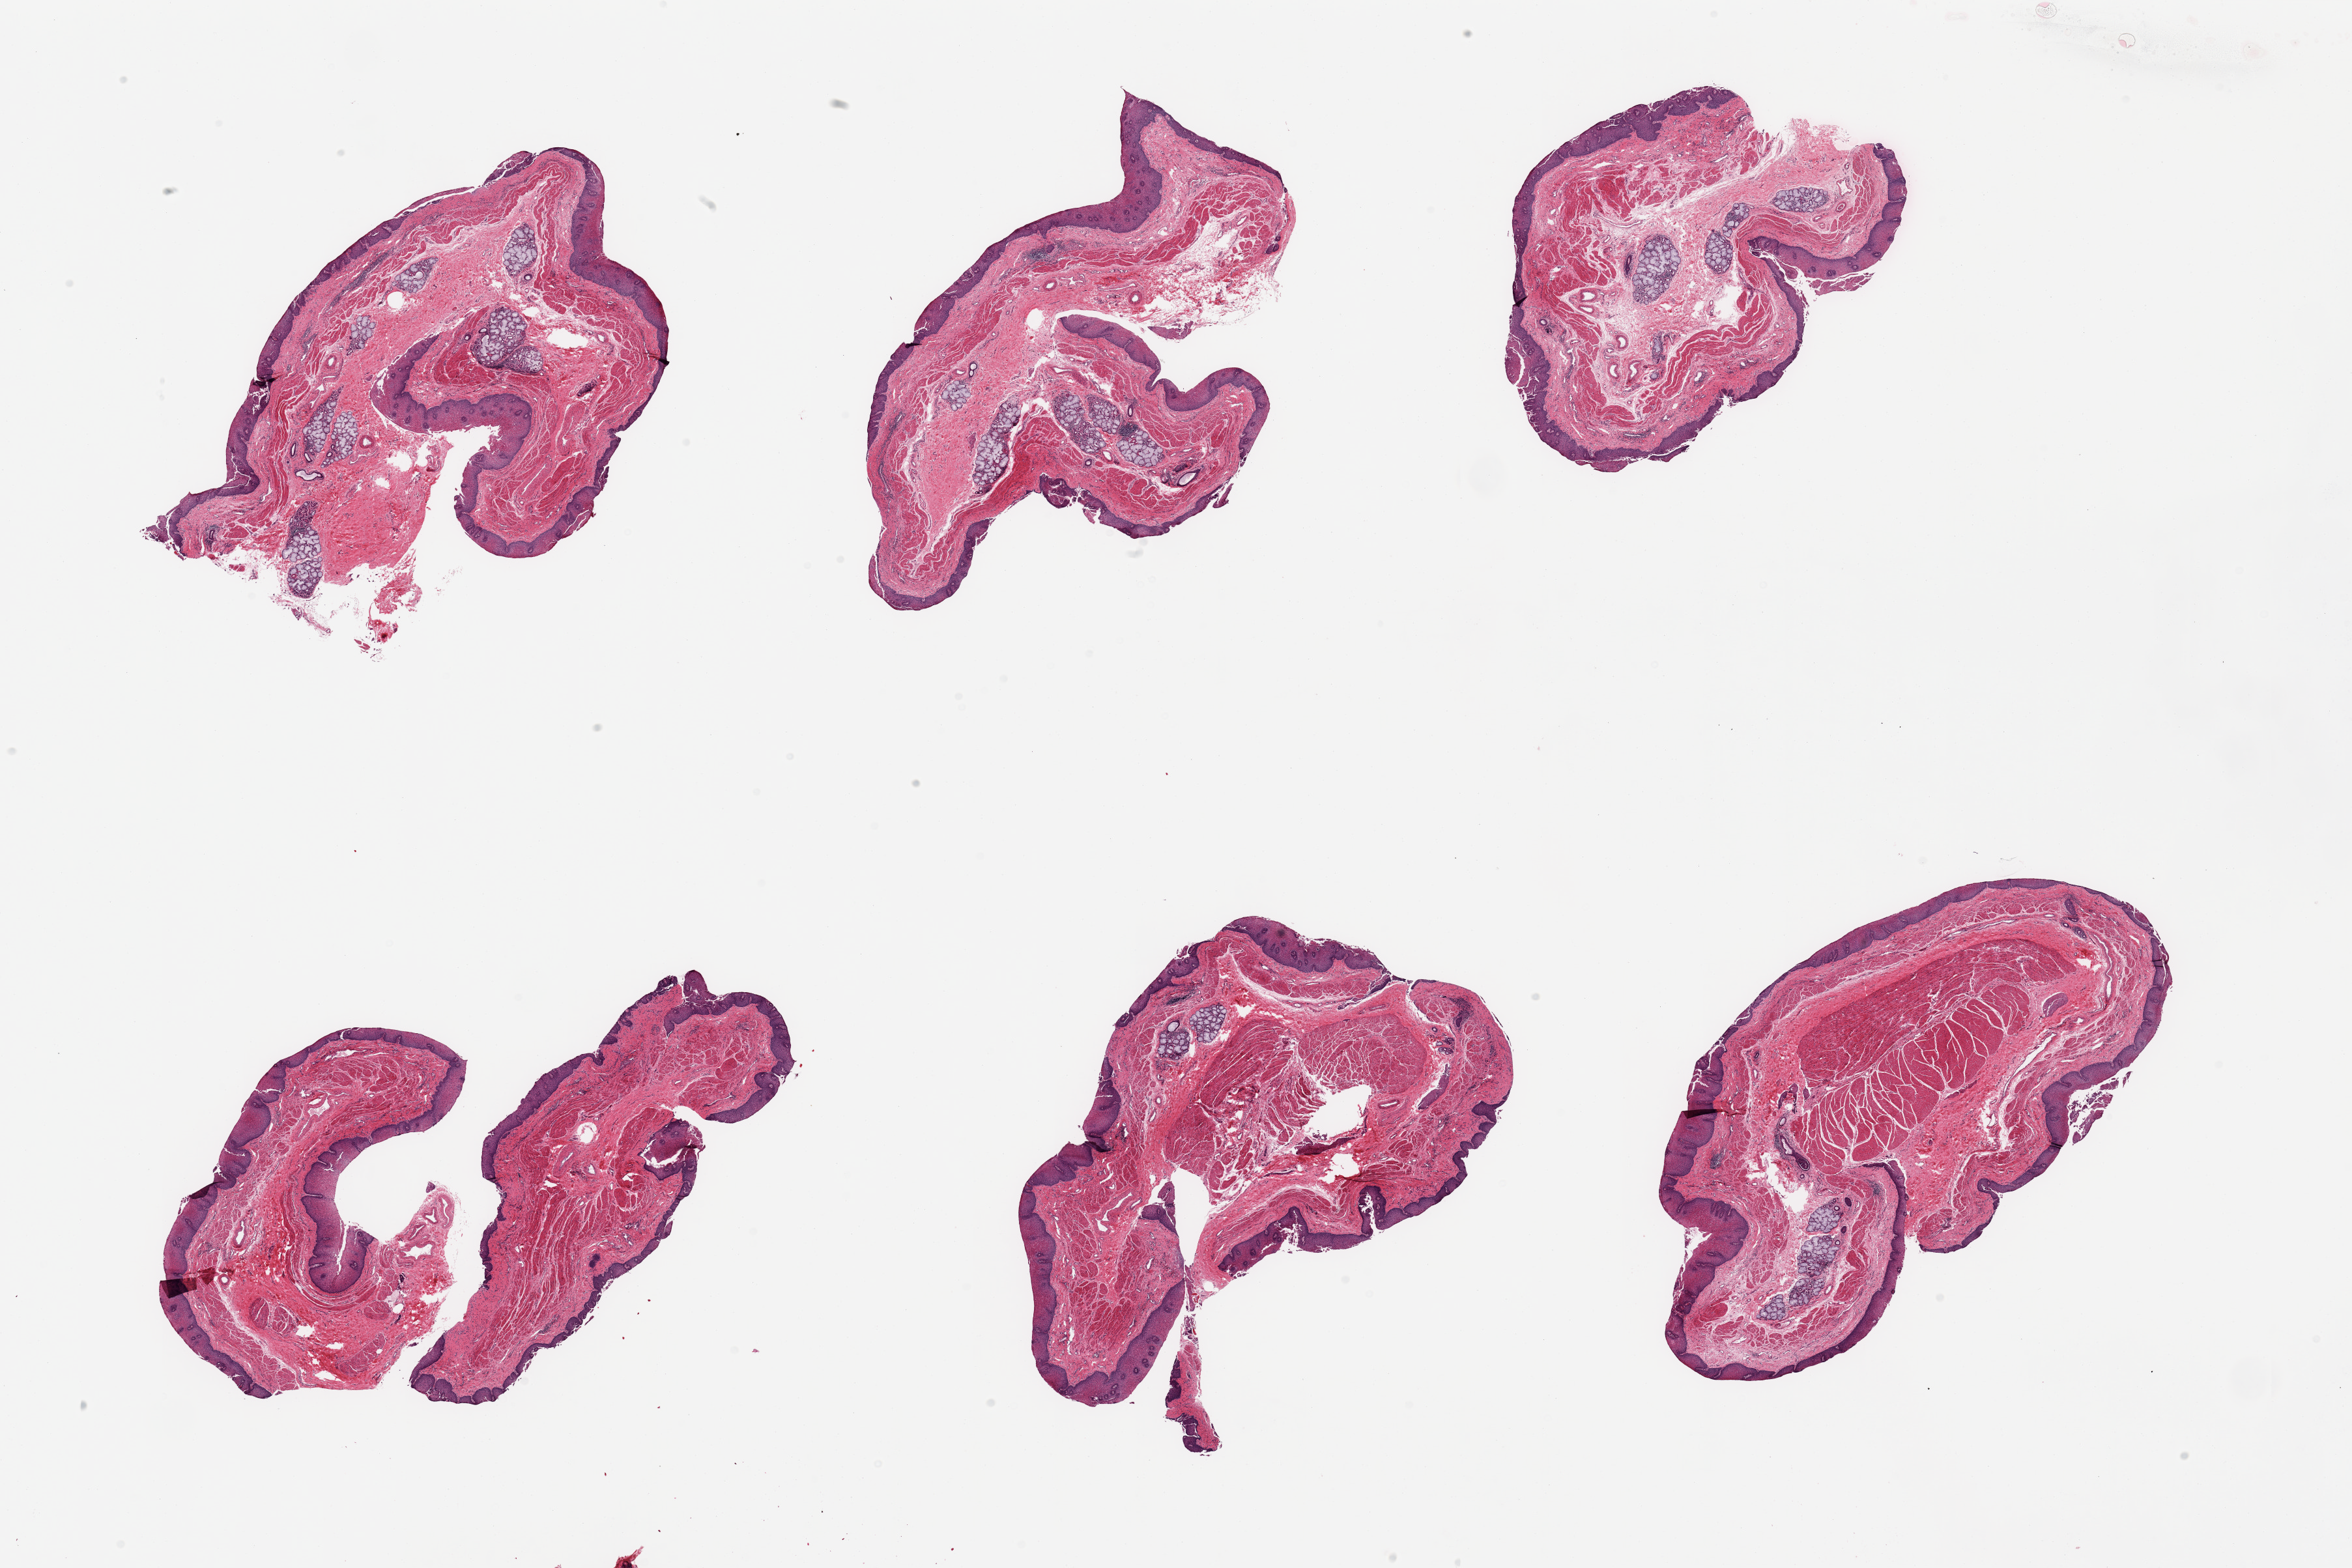
Whole-slide image, H&E stain — shown as a low-resolution overview of the whole scanned area (about 28.5 x 19.0 mm, from a 20x scan). PAXgene-fixed, paraffin-embedded tissue. Target tissue: esophageal mucous membrane. Donor tissue sample.
* review note (as recorded): 6 pieces; 2 of 6 pieces include muscularis propria, many clusters of submucosal glands